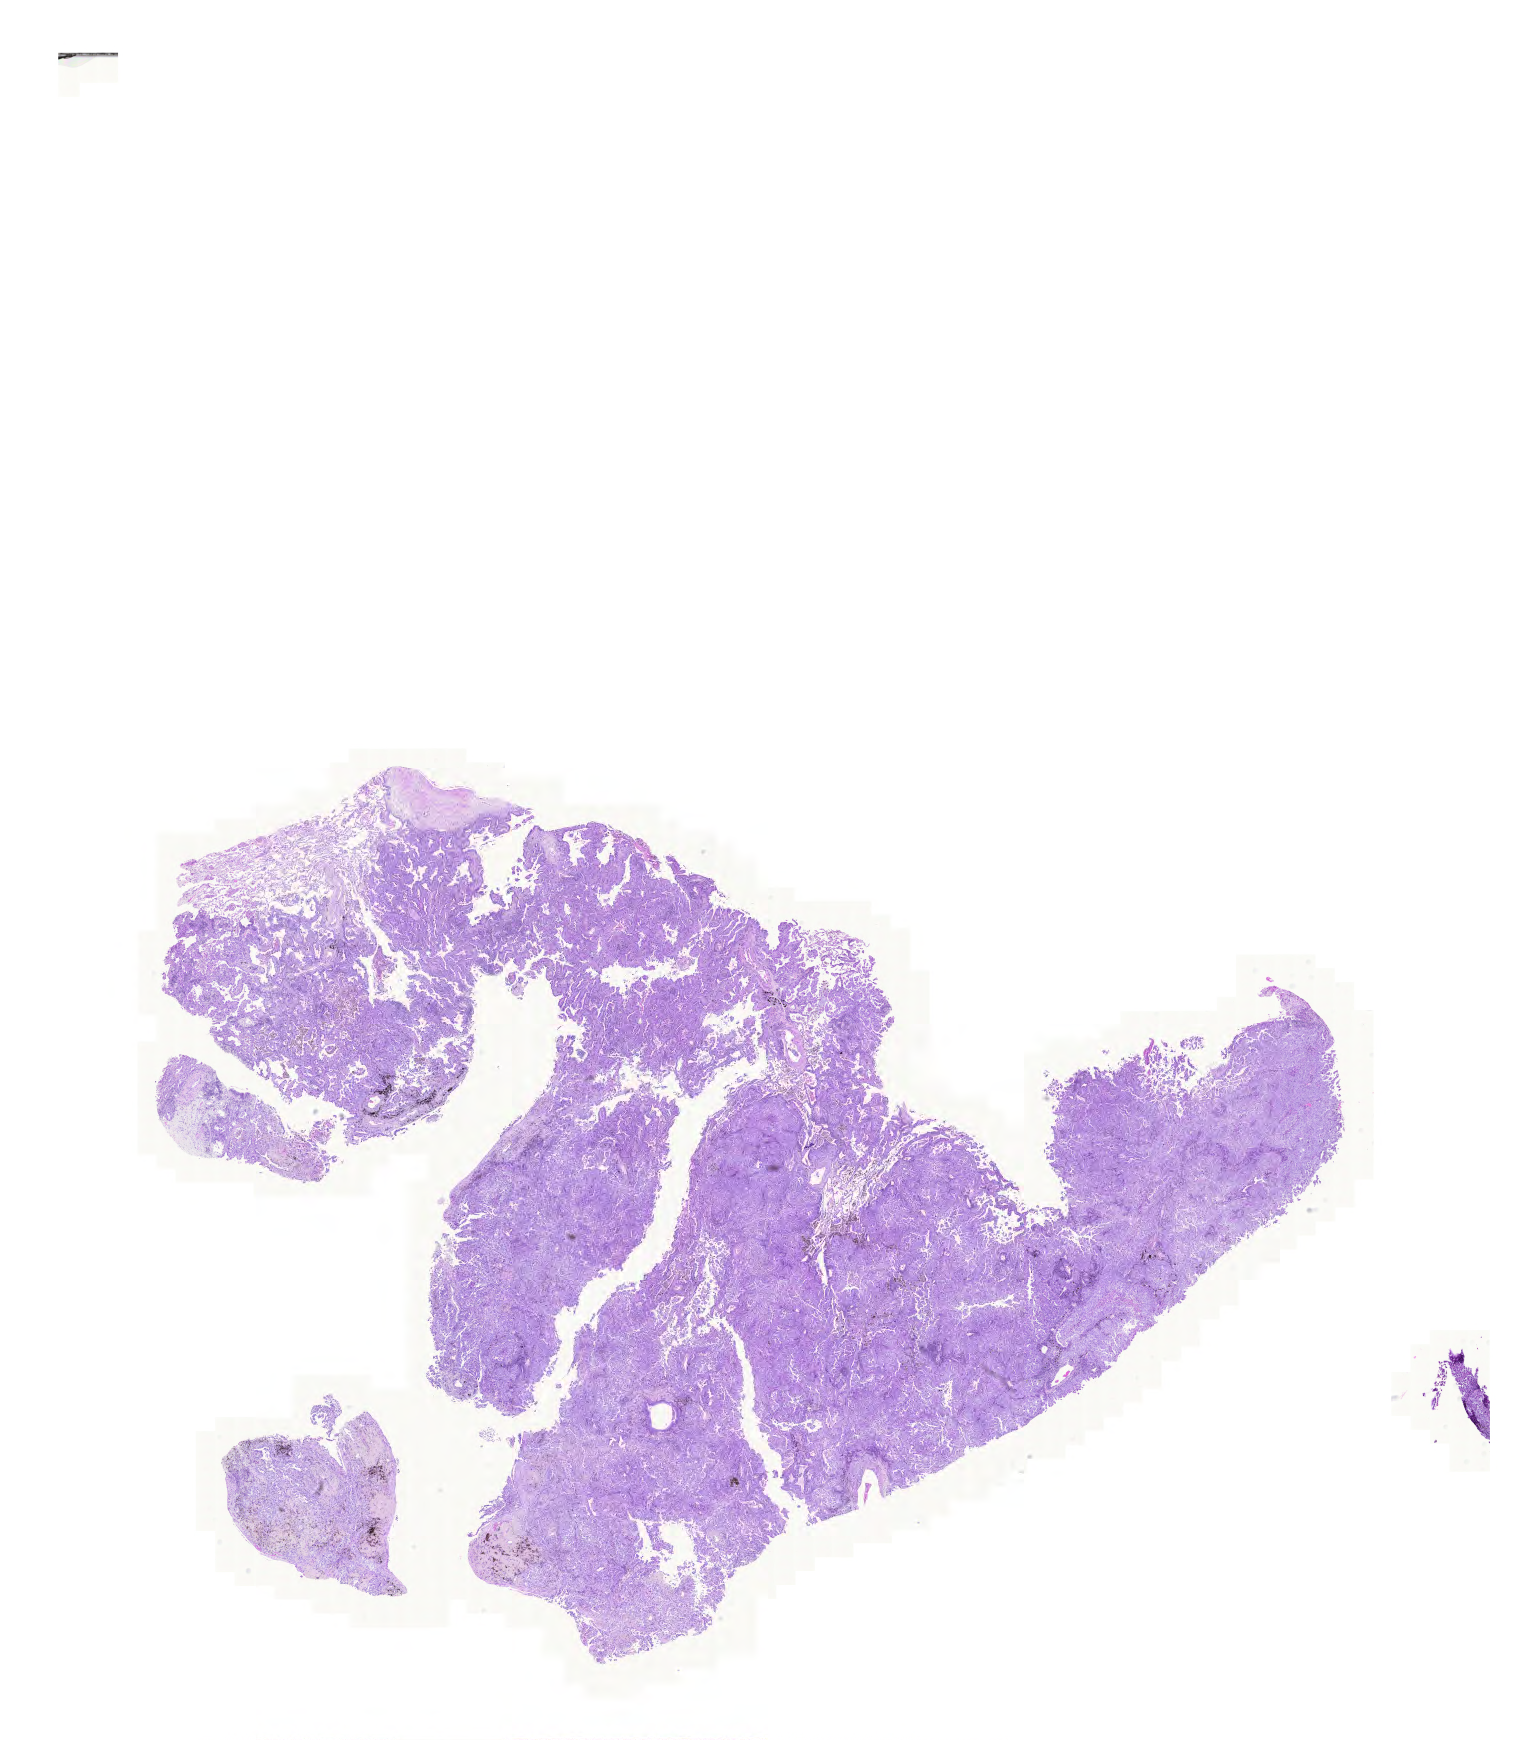
H&E whole-slide image, a low-resolution overview of the entire scanned area, about 22.9 x 25.9 mm. Formalin-fixed paraffin-embedded (FFPE) diagnostic section. Primary tumour sample from the lung. Patient: female, age at initial diagnosis 47 years.
TNM: T4 N3 M0. Laterality: right. Diagnosis: Adenocarcinoma with mixed subtypes (upper lobe, lung). AJCC pathologic stage: IIIB.